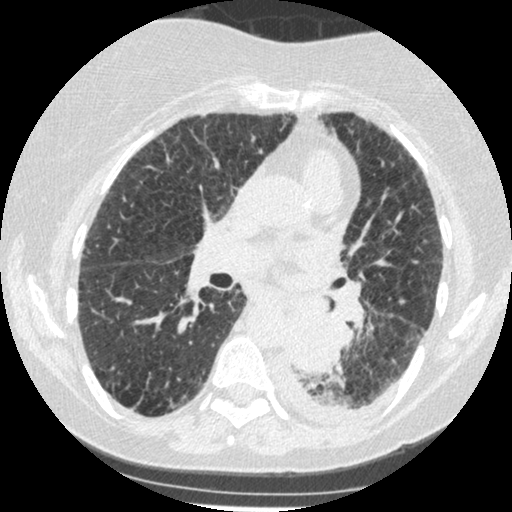
Chest CT (low-dose screening protocol), one axial image. Third annual screen. Lung window (W 1500 / L -600 HU). 1.25 mm slice thickness. 120 kVp. 512 × 512 image matrix. Female, age 60 years at enrolment. Former smoker at enrolment.
• Expert-annotated lung lesion, box from (x=272, y=306) to (x=342, y=374) px.
• Screening reader's record for this exam (one nodule recorded; not confirmed to be the boxed lesion): non-calcified nodule or mass ≥4 mm, left lower lobe, 54 × 38 mm, smooth margins, soft tissue attenuation, pre-existing on the prior screen: yes; interval growth: yes.
• Later outcome: lung cancer diagnosed 15 days after this screen — small cell carcinoma, NOS, left lower lobe, undifferentiated (G4), stage IV (AJCC 6th edition), 69 mm at pathology.